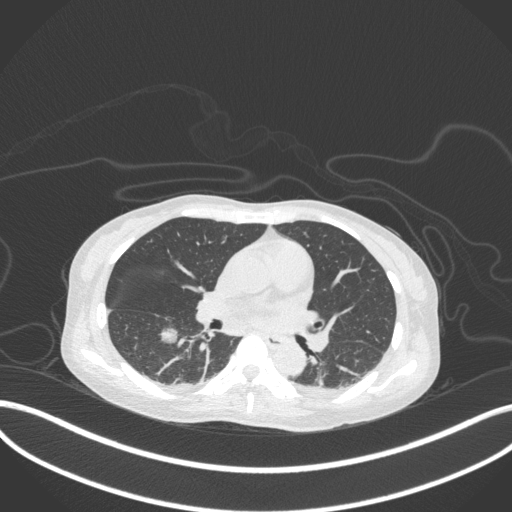
Chest CT, one axial slice; slice 163 of 260 in the series (ordered by position); 120 kVp; lung window (W 1500 / L -600 HU); 1 mm slice thickness; 512 × 512 image matrix. Female patient, age 44 years. Case-level facts recorded for this patient, not image findings: clinical TNM (as recorded): T1c N0 M0.
Structures marked on this image (bounding box drawn by a radiologist):
- lung tumour (recorded histology: adenocarcinoma): box from (x=157, y=321) to (x=181, y=350) px